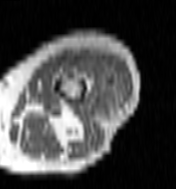
MRI of an extremity soft-tissue mass, one axial slice; MR volume resampled by the dataset authors to the PET/CT grid (not the native acquisition matrix); 176 × 189 image matrix, field of view 172 × 185 mm. Female patient. From the clinical record (not read from this slice): histological type: undifferentiated – high grade; grade: high; site of the primary tumour: left thigh.
Annotated regions visible in this slice (expert contour drawn on MRI and transferred to this co-registered scan by the dataset authors):
- gross tumour volume including surrounding oedema: bounding box (x1, y1, x2, y2) in pixels: (64, 55, 122, 106)